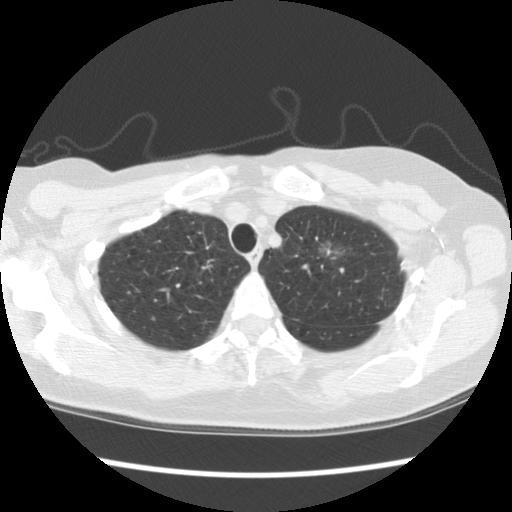
Low-dose screening chest CT, axial slice, second screening round (one year after baseline), lung window (W 1500 / L -600 HU), slice 89 of 110 in the series. Female, age 65 years at enrolment. Former smoker at enrolment.
Expert reader's lesion annotation, box from (x=298, y=224) to (x=365, y=284) px. The screening reader recorded 2 non-calcified nodules or masses ≥4 mm on this exam (right upper lobe, left upper lobe); which of them this box marks is not recorded. Official screen result: positive, other.